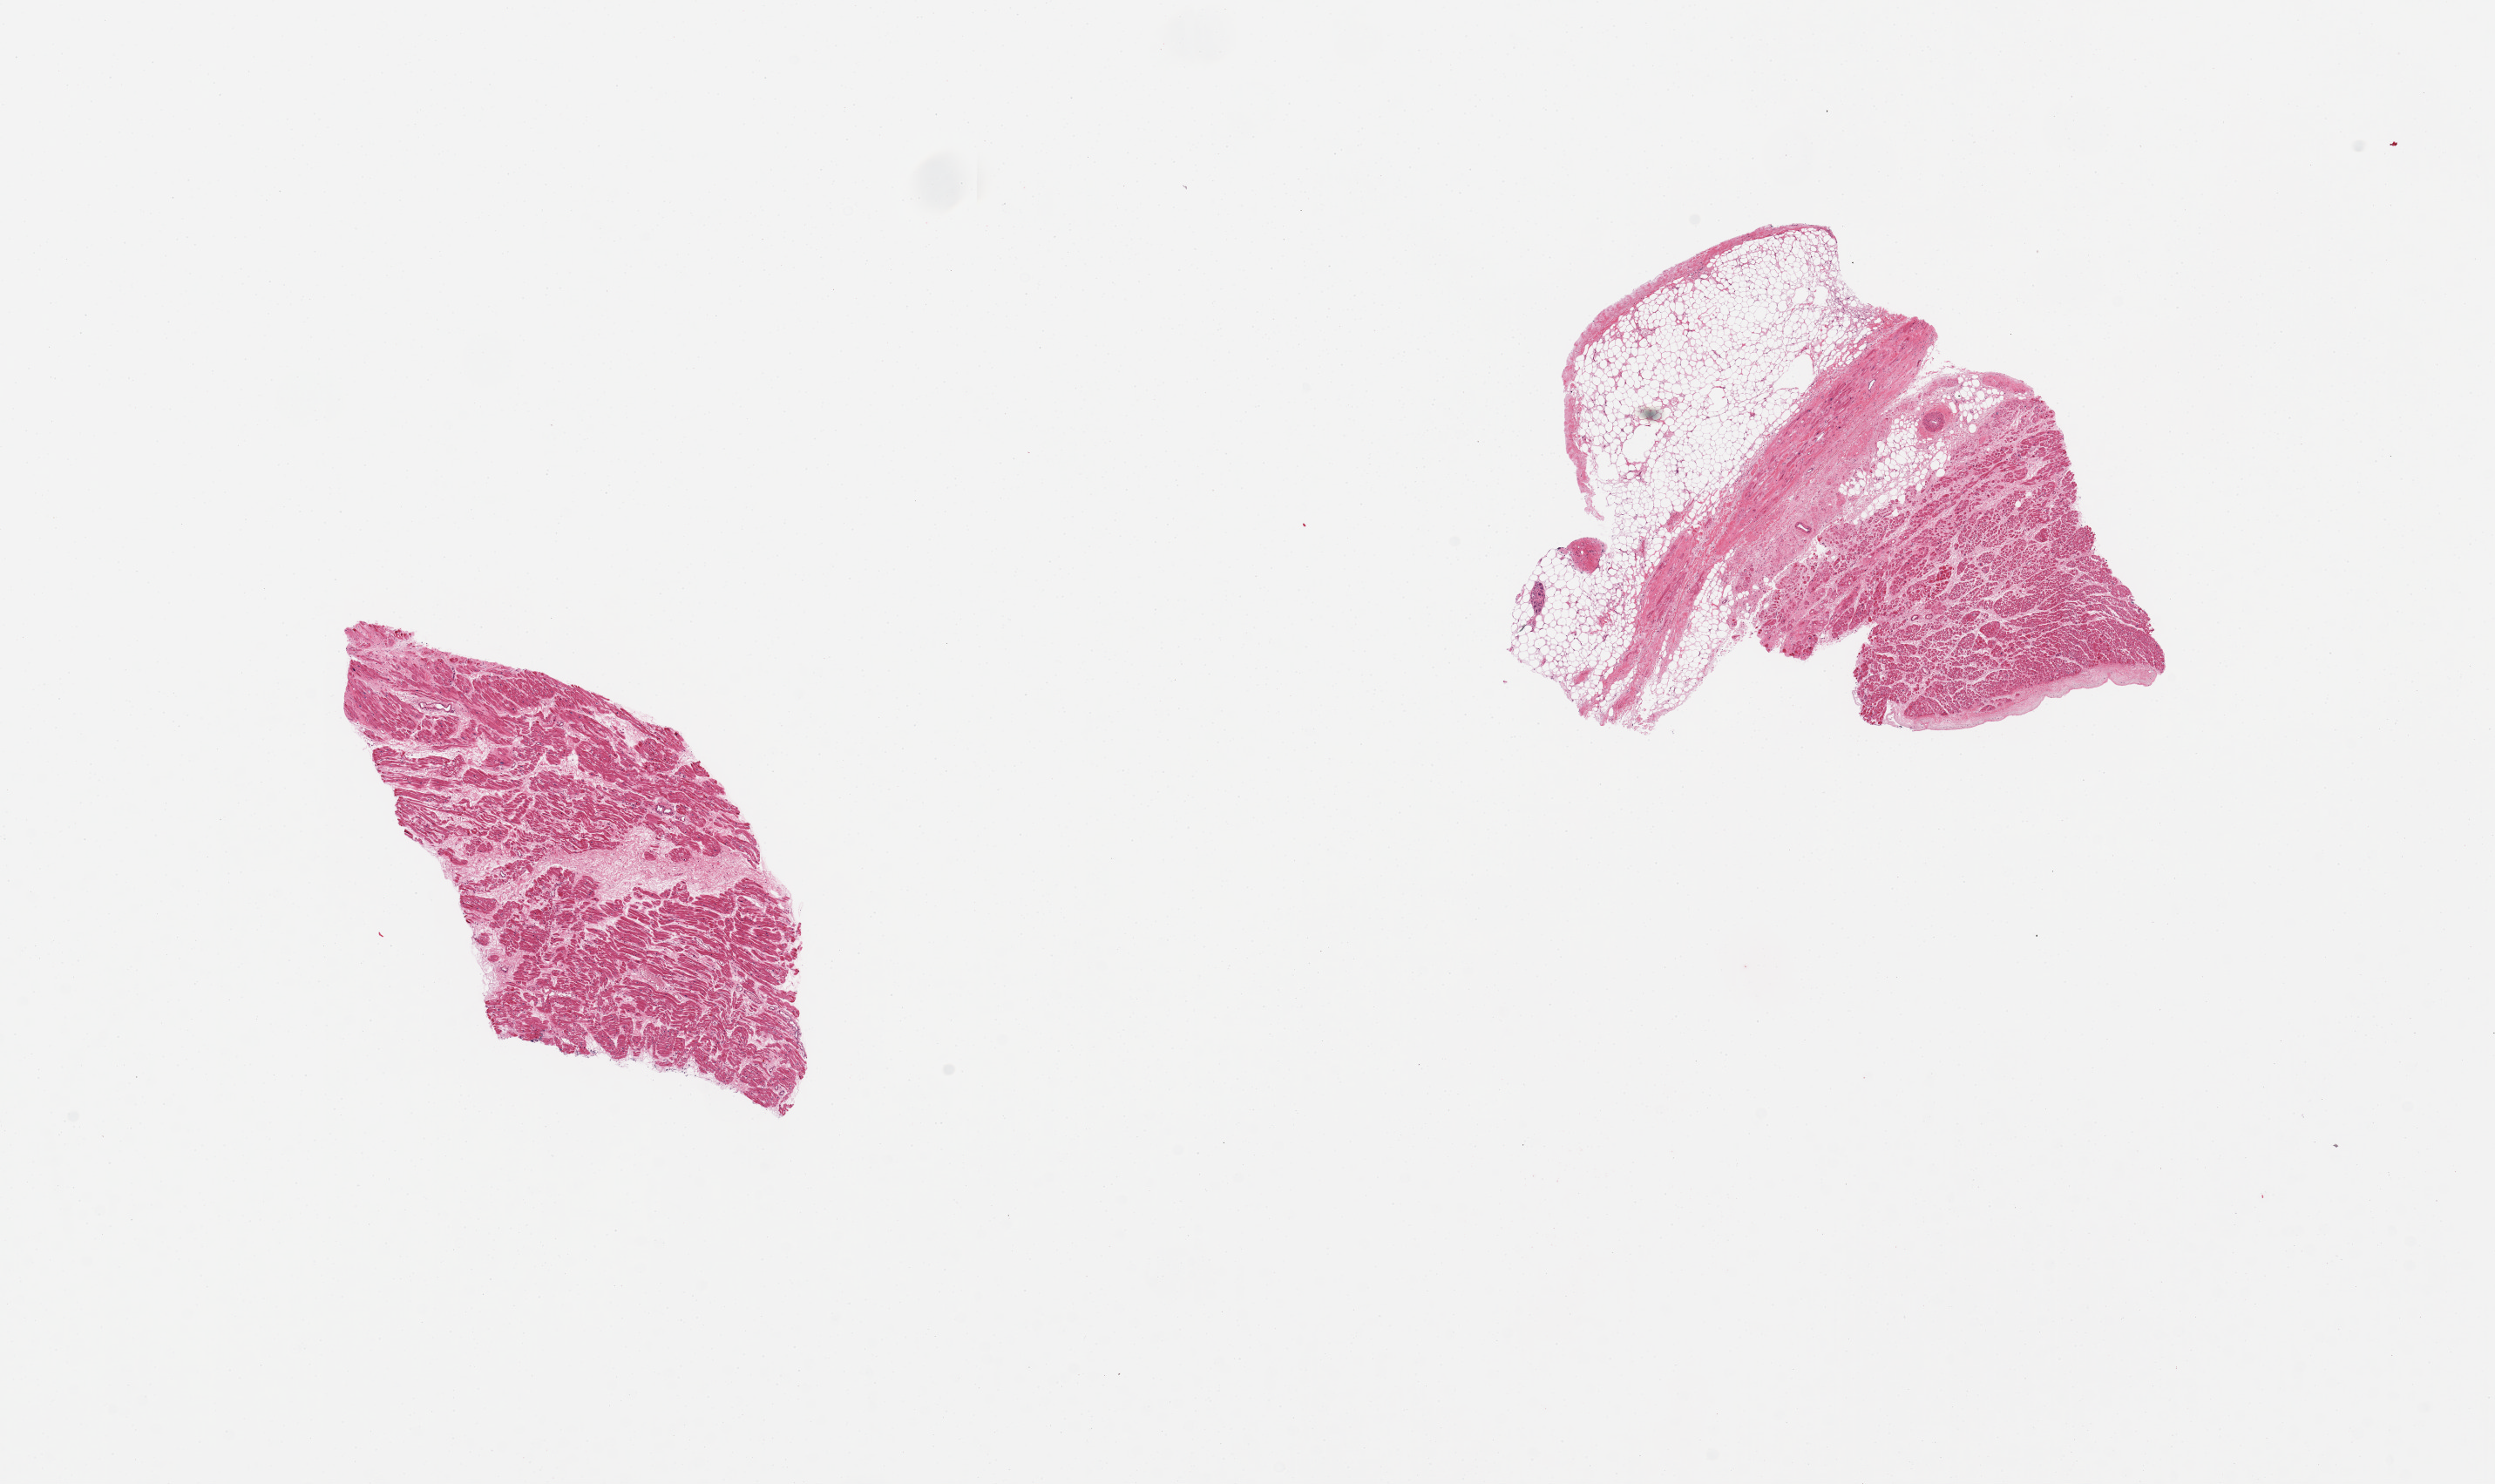
Digitized hematoxylin and eosin (H&E)-stained section — whole scanned area (about 22.6 x 13.5 mm) shown as a low-resolution overview. PAXgene-fixed paraffin-embedded (PFPE) section. Sampled site (target tissue): auricular appendage. Donor tissue sample. Male donor.
- review note (as recorded): 2 pieces, 1 with 50% external fat; hypertrophied myofibers